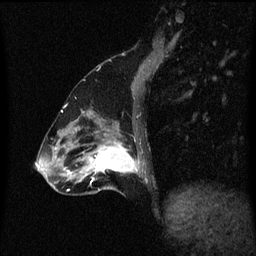
Breast MRI (dynamic contrast-enhanced), one sagittal slice; position 22 of 60 along the scan axis; dynamic contrast-enhanced series, image 2 of 3 at this slice position (ordered by acquisition); 1.5 T; TE 4.2 ms, TR 8.4 ms; 2 mm slice thickness; 256 × 256 image matrix. Patient: female, 47 years.
Structures marked on this image (semi-automatically segmented with operator editing):
- analysis volume of interest (the breast-tissue region the enhancement analysis was run in; not a lesion): bounding box <85,136,143,195> (left, top, right, bottom; pixels)
- tumour enhancement mask (voxels above the 70 % enhancement threshold inside the analysis volume of interest): <91,142,140,181>